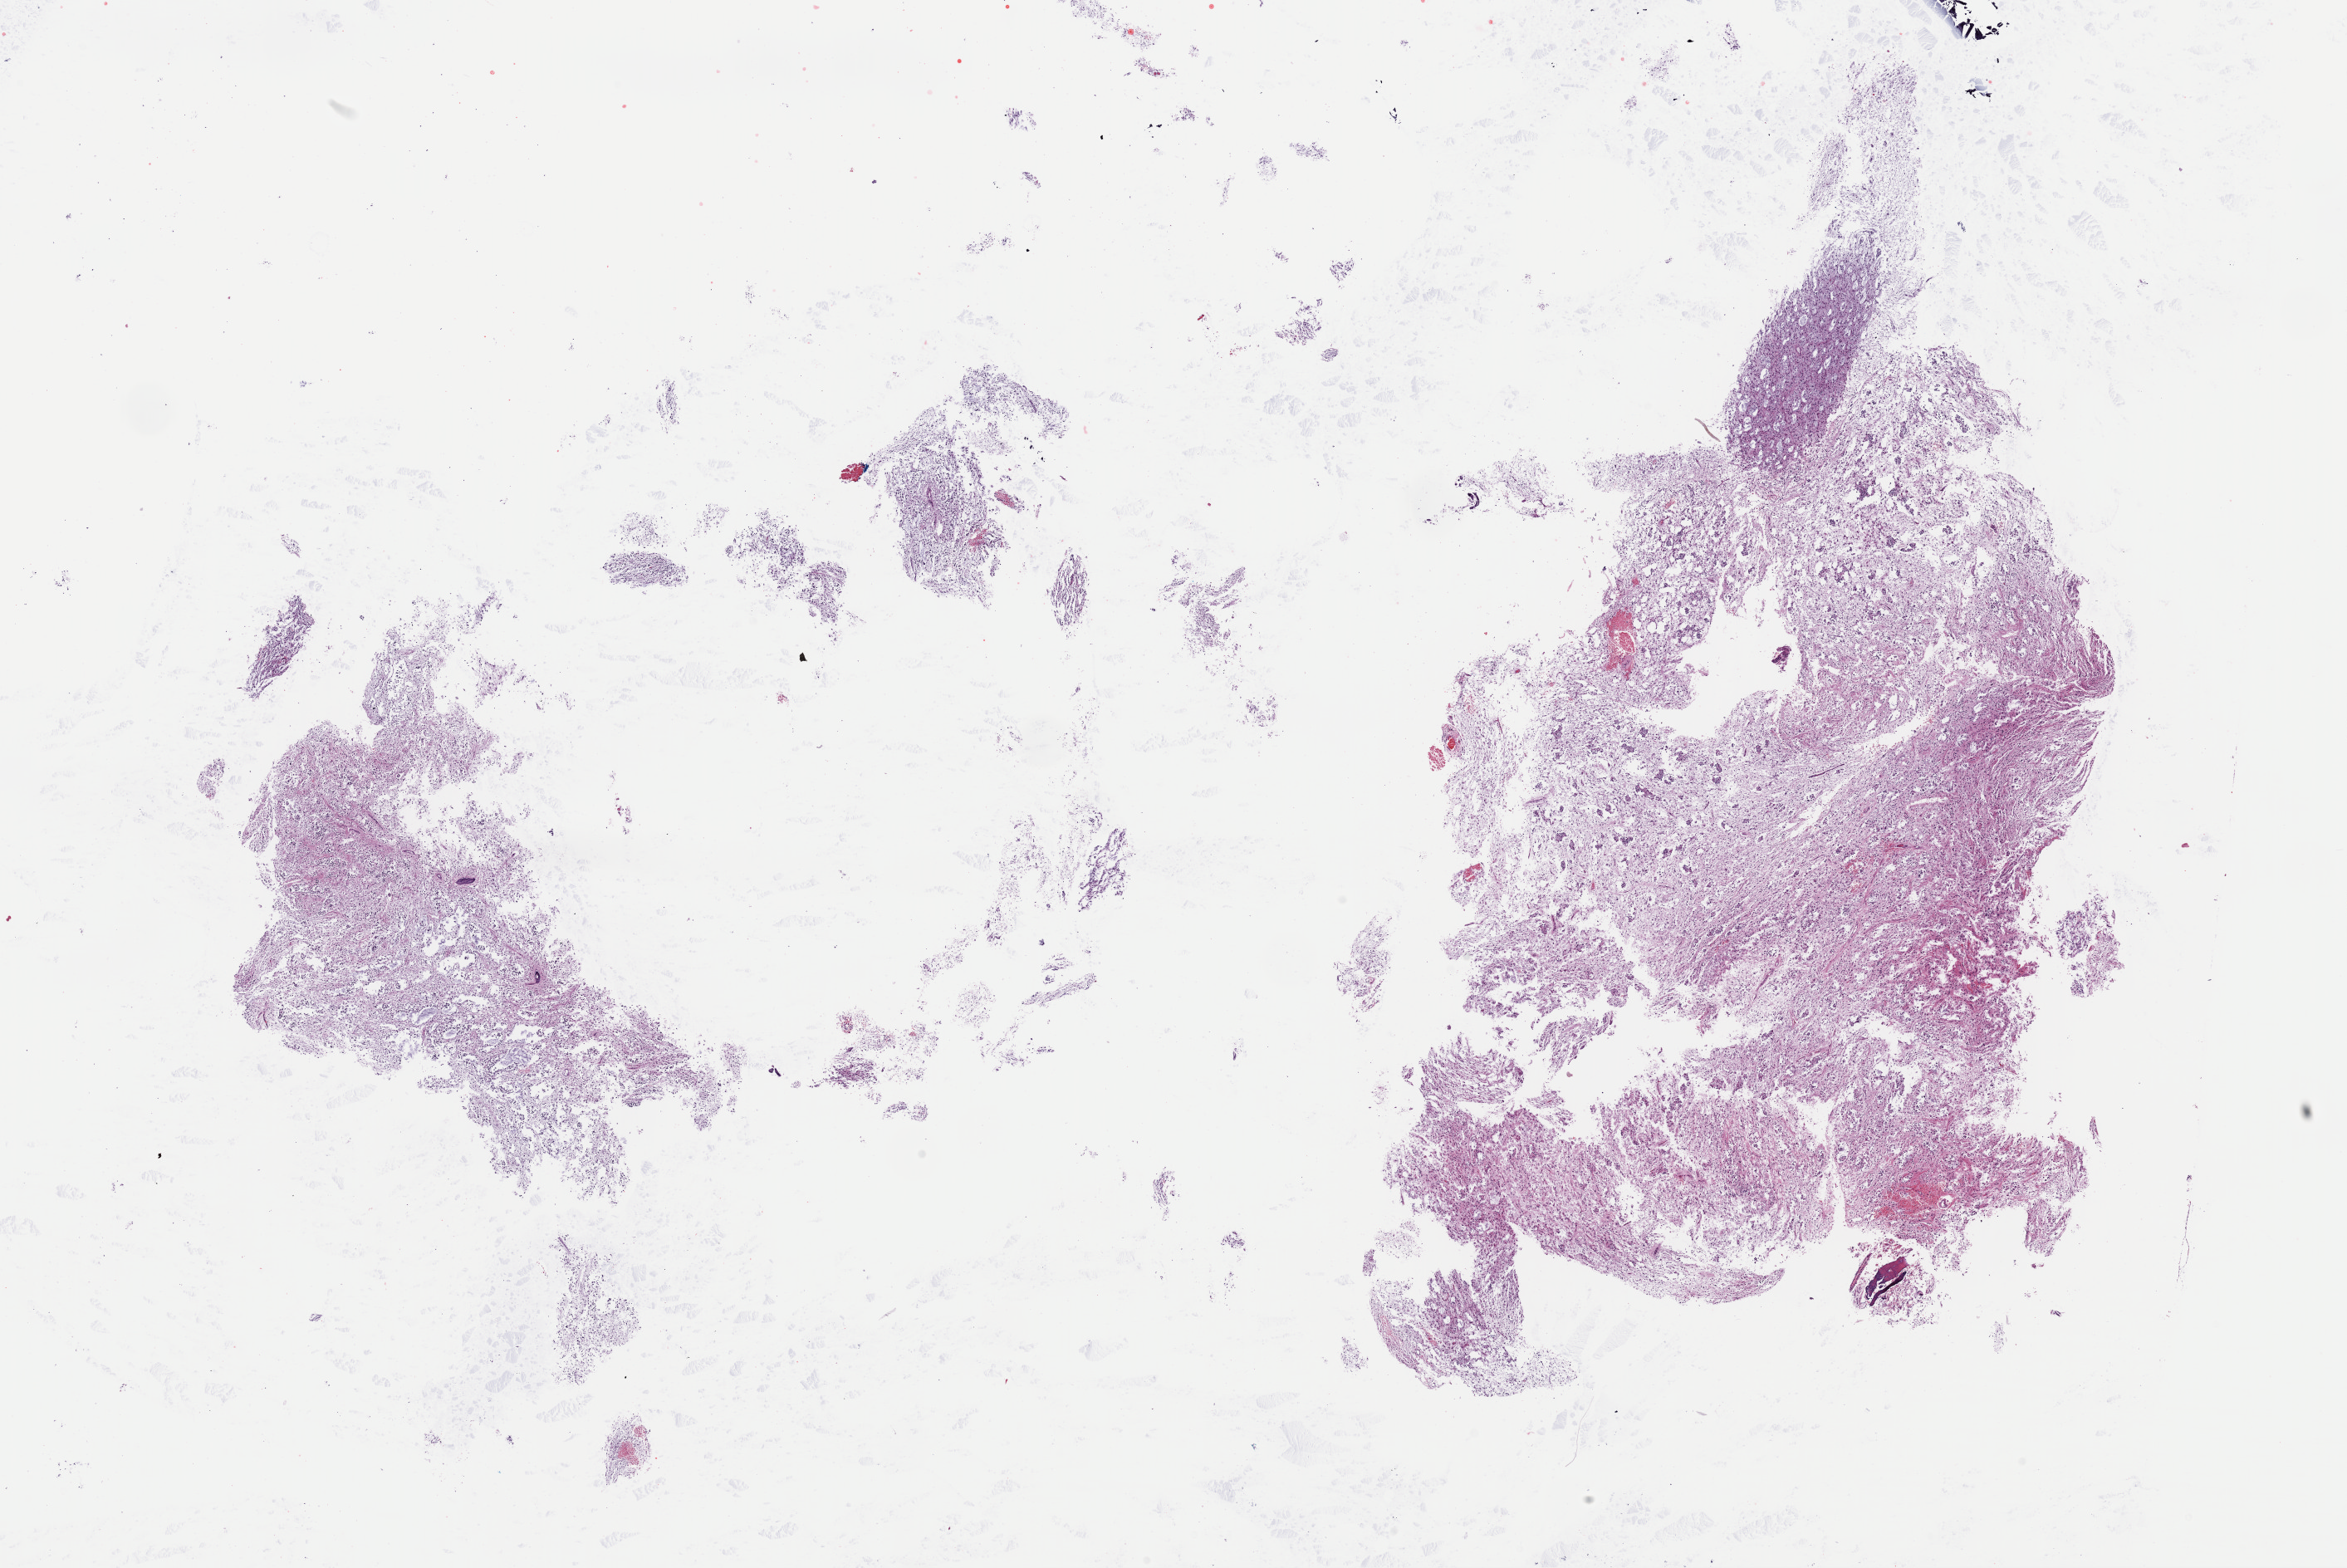
Whole-slide histology image, Hematoxylin and eosin (H&E) stained — a low-resolution overview of the entire scanned area, about 22.3 x 14.9 mm (from a 40x scan), formalin-fixed paraffin-embedded (FFPE) diagnostic section, brain, primary tumour sample. Patient: male, age at initial diagnosis 35 years. Histologic grade: G2 (moderately differentiated).
Histologic diagnosis: Astrocytoma, NOS (cerebrum).